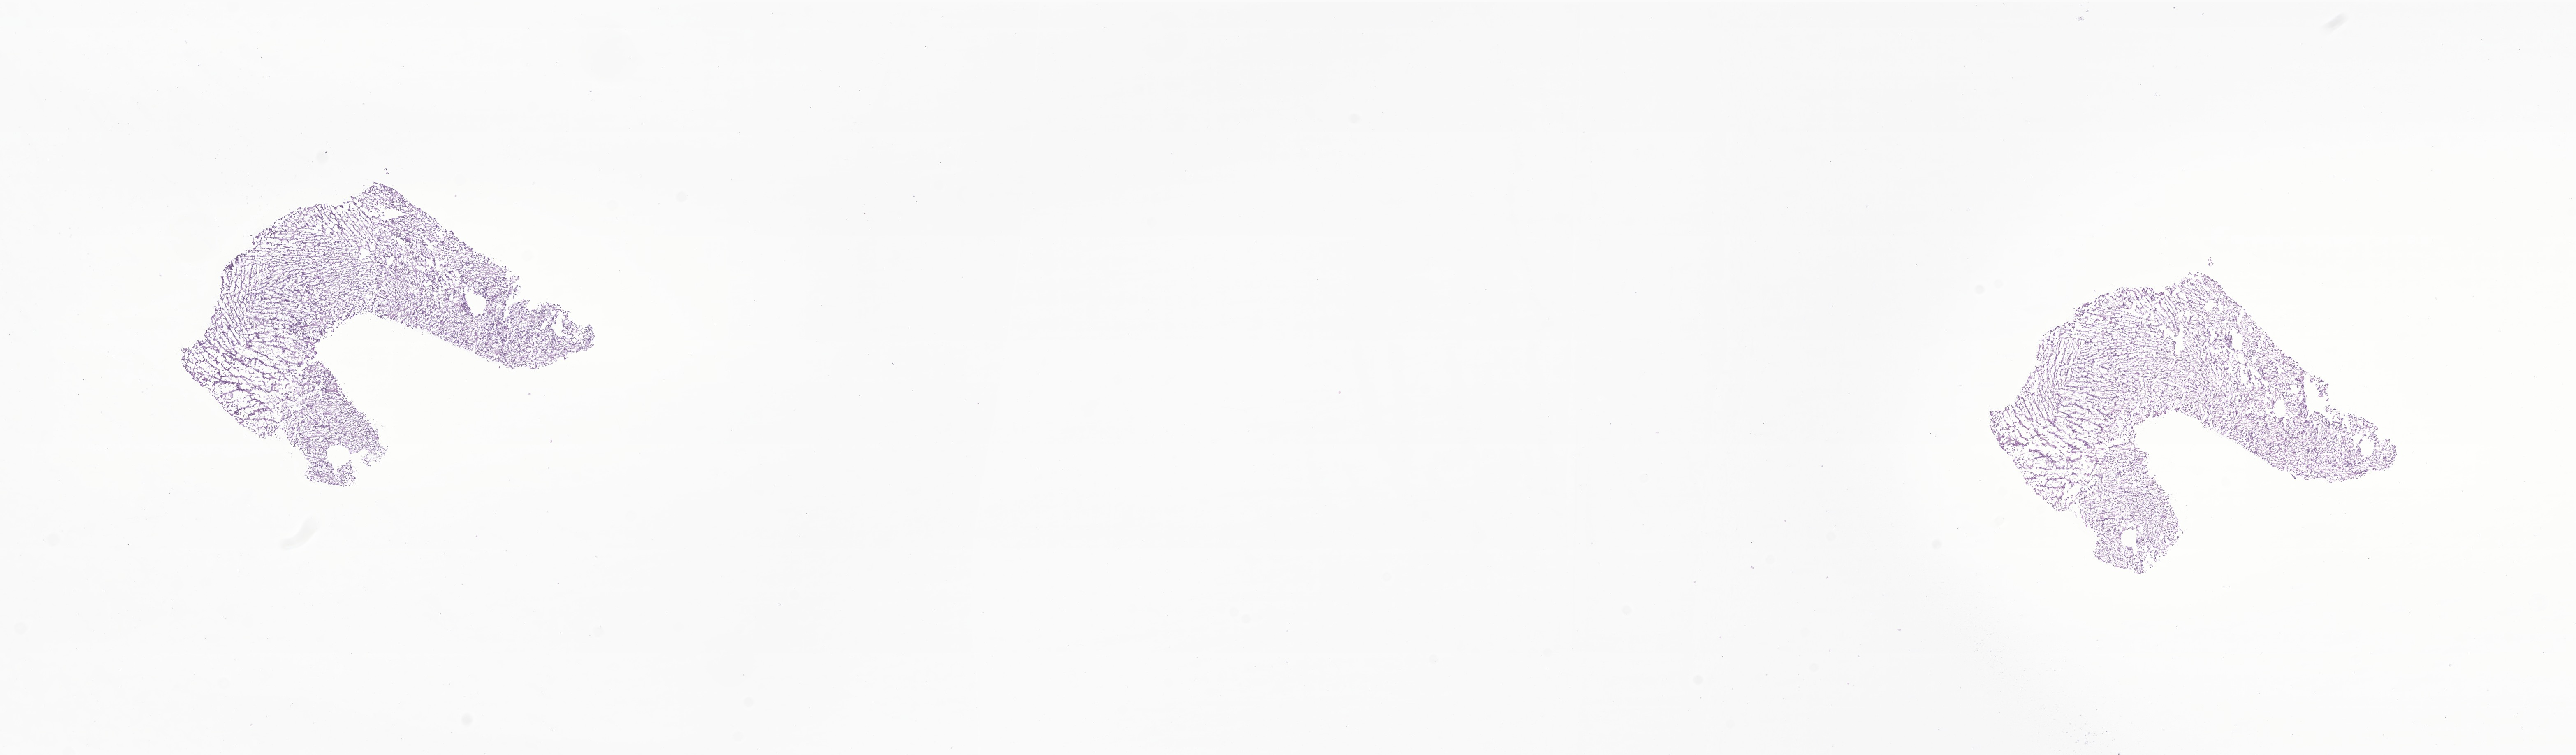
H&E whole-slide image of tumor tissue from the brain, whole scanned area (about 26.4 x 7.7 mm) shown as a low-resolution overview. Cryosection (OCT / tissue freezing medium). Female patient, age 53 months (4 years 5 months).
Diagnosis (ICD-O-3 morphology term): Ependymoma, NOS.